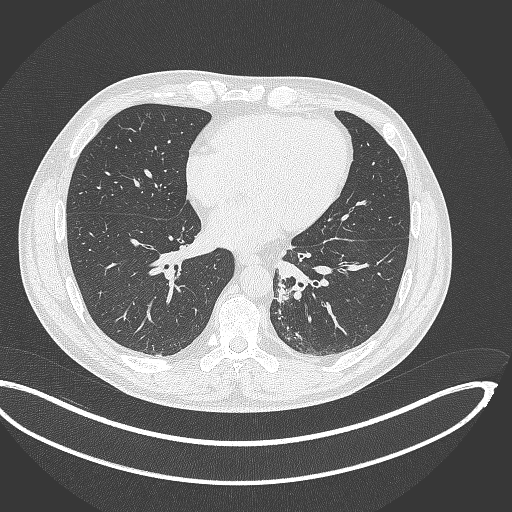
Chest CT, one axial slice. Position 138 of 362 along the scan axis. Lung window (W 1500 / L -600 HU). 512 × 512 image matrix, field of view 442 × 442 mm. Patient: male, 50 years. From the clinical record (not read from this slice): clinical TNM (as recorded): T2a N3 M0.
Annotated regions visible in this slice (bounding box drawn by a radiologist):
- lung tumour (recorded histology: squamous cell carcinoma): bounding box [x1, y1, x2, y2] px = [273, 279, 292, 306]